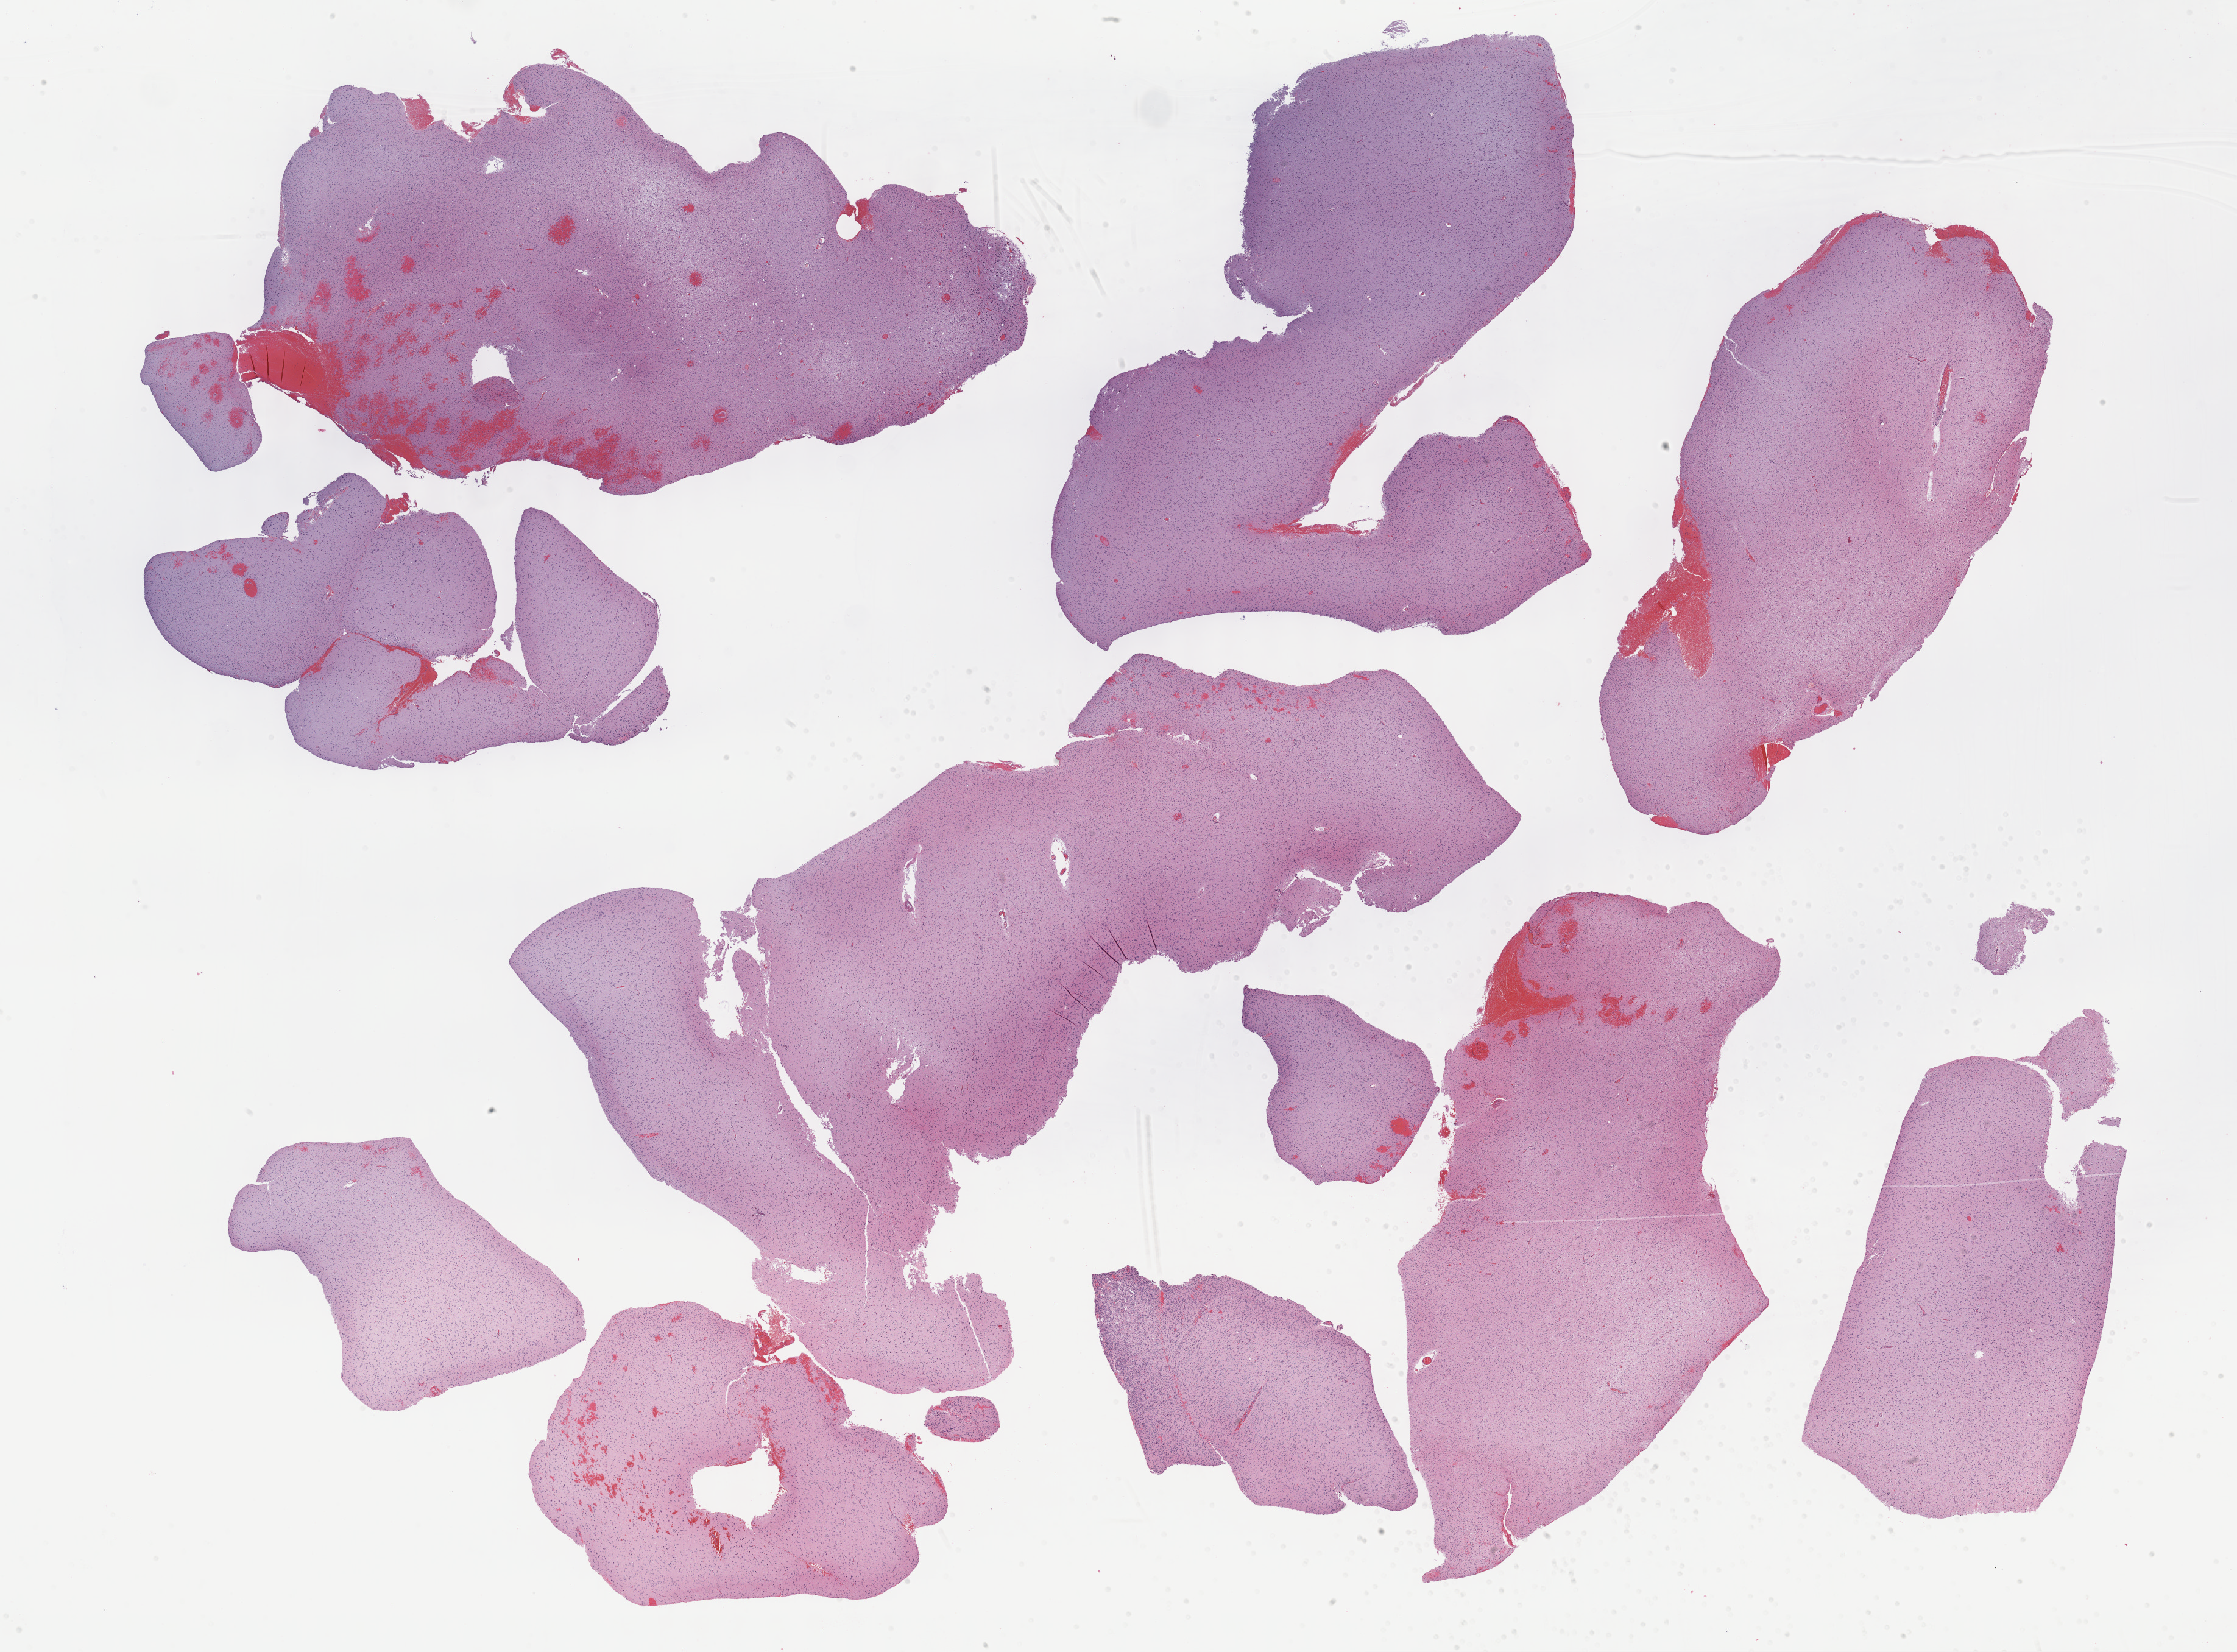
H&E-stained whole-slide image, a low-resolution overview of the entire scanned area, about 29.7 x 21.9 mm (acquisition: 40x scan); FFPE section; brain, primary tumour sample. Patient: male, age at initial diagnosis 54 years. Histologic grade: G2 (moderately differentiated).
Pathologic diagnosis: Oligodendroglioma, NOS (cerebrum).